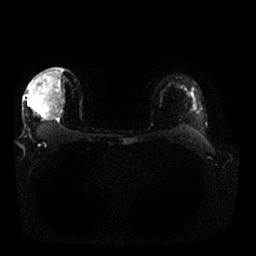
Breast MRI, one axial slice; position 15 of 25 along the scan axis; diffusion-weighted series; image 2 of 4 stored at this slice position (different b-values; order by instance number); 1.5 T; 256 × 256 image matrix. Female patient.
Structures marked on this image (expert manual segmentation):
- tumour on diffusion-weighted imaging: bounding box [x1, y1, x2, y2] px = [57, 113, 61, 118]